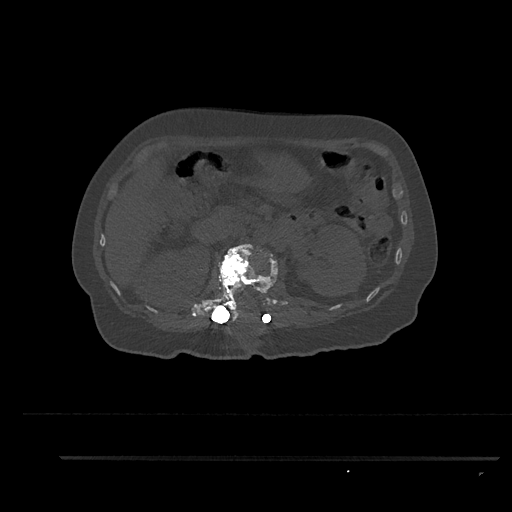
CT including the spine, one axial slice. Position 207 of 797 along the scan axis. Reconstruction kernel Br40s/3. 120 kVp. Bone window (W 1800 / L 400 HU). 0.5 mm slice thickness. 512 × 512 image matrix, field of view 408 × 408 mm. Patient: female, 44 years. Case-level facts recorded for this patient, not image findings: primary cancer: renal; vertebrae with lytic lesions (as recorded): L1.
Annotated regions visible in this slice (semi-automatic segmentation, software-assisted and operator-edited):
- L1 vertebra: bounding box (x1, y1, x2, y2) in pixels: (203, 244, 278, 322)